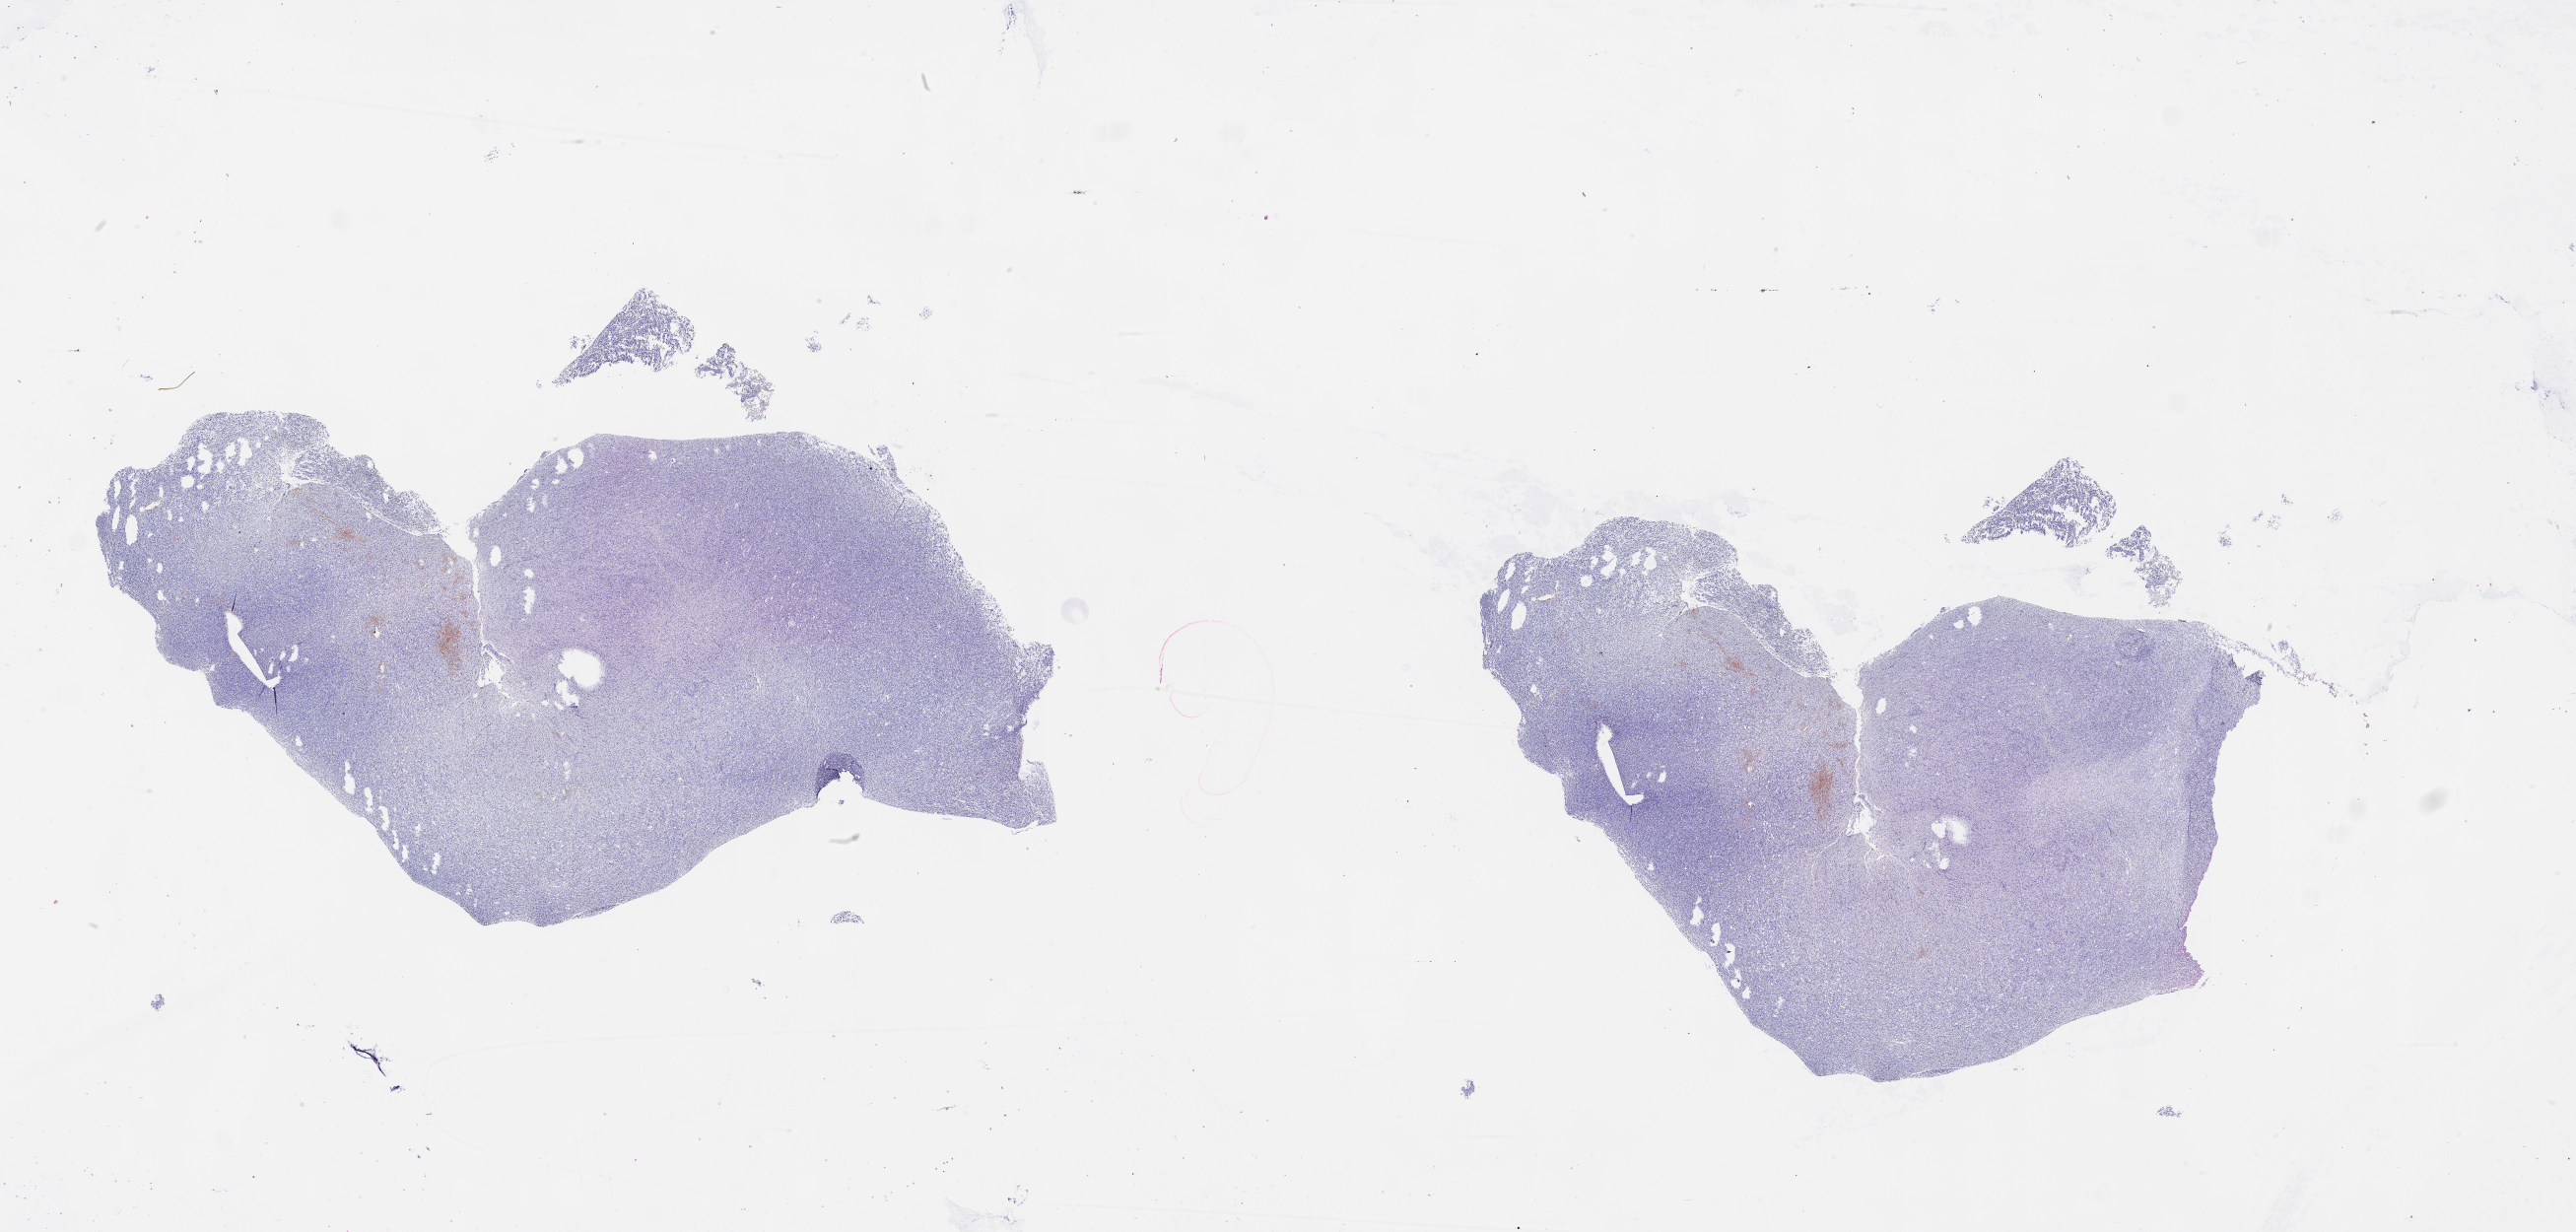
Whole-slide histology image, Hematoxylin and eosin (H&E) stained, whole scanned area (about 42.1 x 20.1 mm, acquisition: 20x scan) shown as a low-resolution overview, tumour tissue sample, brain. Patient: male, age 36 years.
- diagnosis: Glioblastoma
- primary tumour site (as recorded): frontal lobe